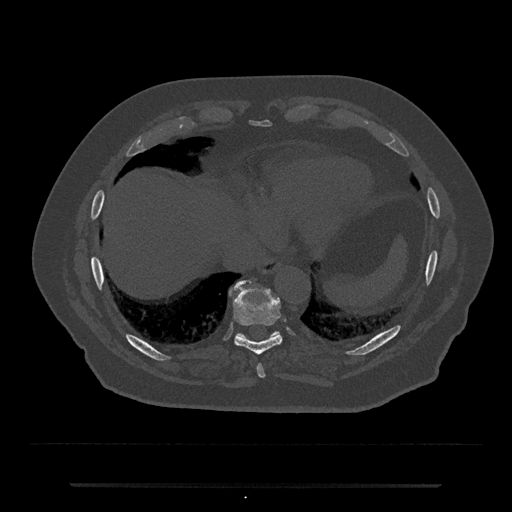
CT including the spine, one axial slice. Position 748 of 797 along the scan axis. Bone window (W 1800 / L 400 HU). 0.5 mm slice thickness. 512 × 512 image matrix. Male patient, age 80 years. From the clinical record (not read from this slice): primary cancer: prostate.
Structures marked on this image (semi-automatic segmentation, software-assisted and operator-edited):
- T10 vertebra: bounding box [x1, y1, x2, y2] px = [230, 289, 280, 339]
- T8 vertebra: [257, 364, 265, 378]
- T9 vertebra: [234, 285, 282, 355]